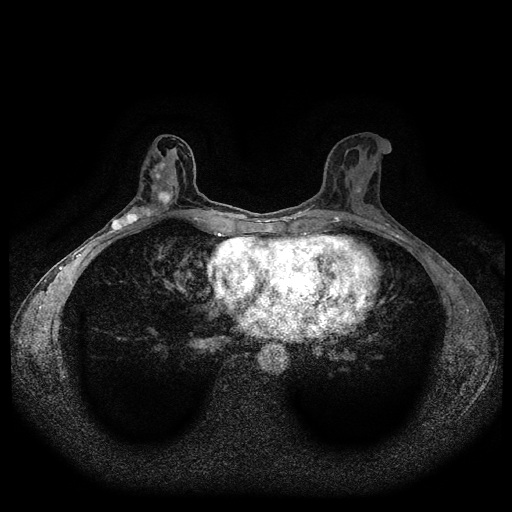
Breast MRI (dynamic contrast-enhanced, multi-phase), one axial slice; position 50 of 116 along the scan axis; dynamic contrast-enhanced series, time point 2 of 5 at this slice position (early post-contrast); 1.5 T; TE 2.6 ms, TR 5.3 ms; 2 mm slice thickness; 512 × 512 image matrix. Female patient, age 50 years.
Structures marked on this image (semi-automatically segmented with operator editing):
- breast lesion (labelled 'tumour' in the annotation; benign lesions carry a separate 'benign' label): bounding box (x1, y1, x2, y2) in pixels: (111, 190, 174, 230)